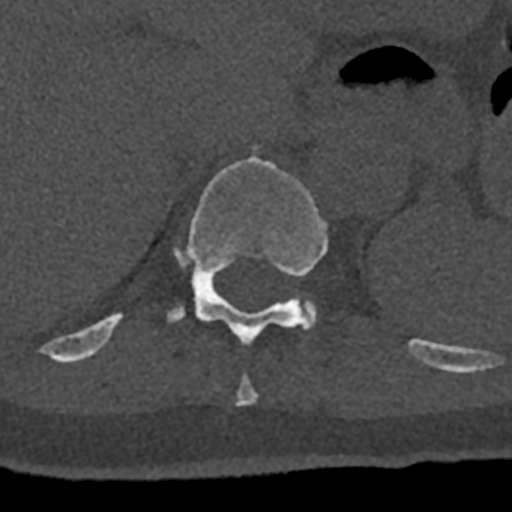
CT including the spine, one axial slice. Slice 546 of 797 in the series (ordered by position). Reconstruction kernel Br40s/3. 120 kVp. Bone window (W 1800 / L 400 HU). 0.5 mm slice thickness. 512 × 512 image matrix, field of view 160 × 160 mm. Patient: male, 74 years. From the clinical record (not read from this slice): primary cancer: renal; vertebrae with lytic lesions (as recorded): T10, L1, L2, L3, L4, L5.
Annotated regions visible in this slice (semi-automatic segmentation, software-assisted and operator-edited):
- T10 vertebra: bounding box (x1, y1, x2, y2) in pixels: (235, 374, 258, 406)
- T11 vertebra: (70, 145, 432, 366)
- T12 vertebra: (303, 300, 316, 327)